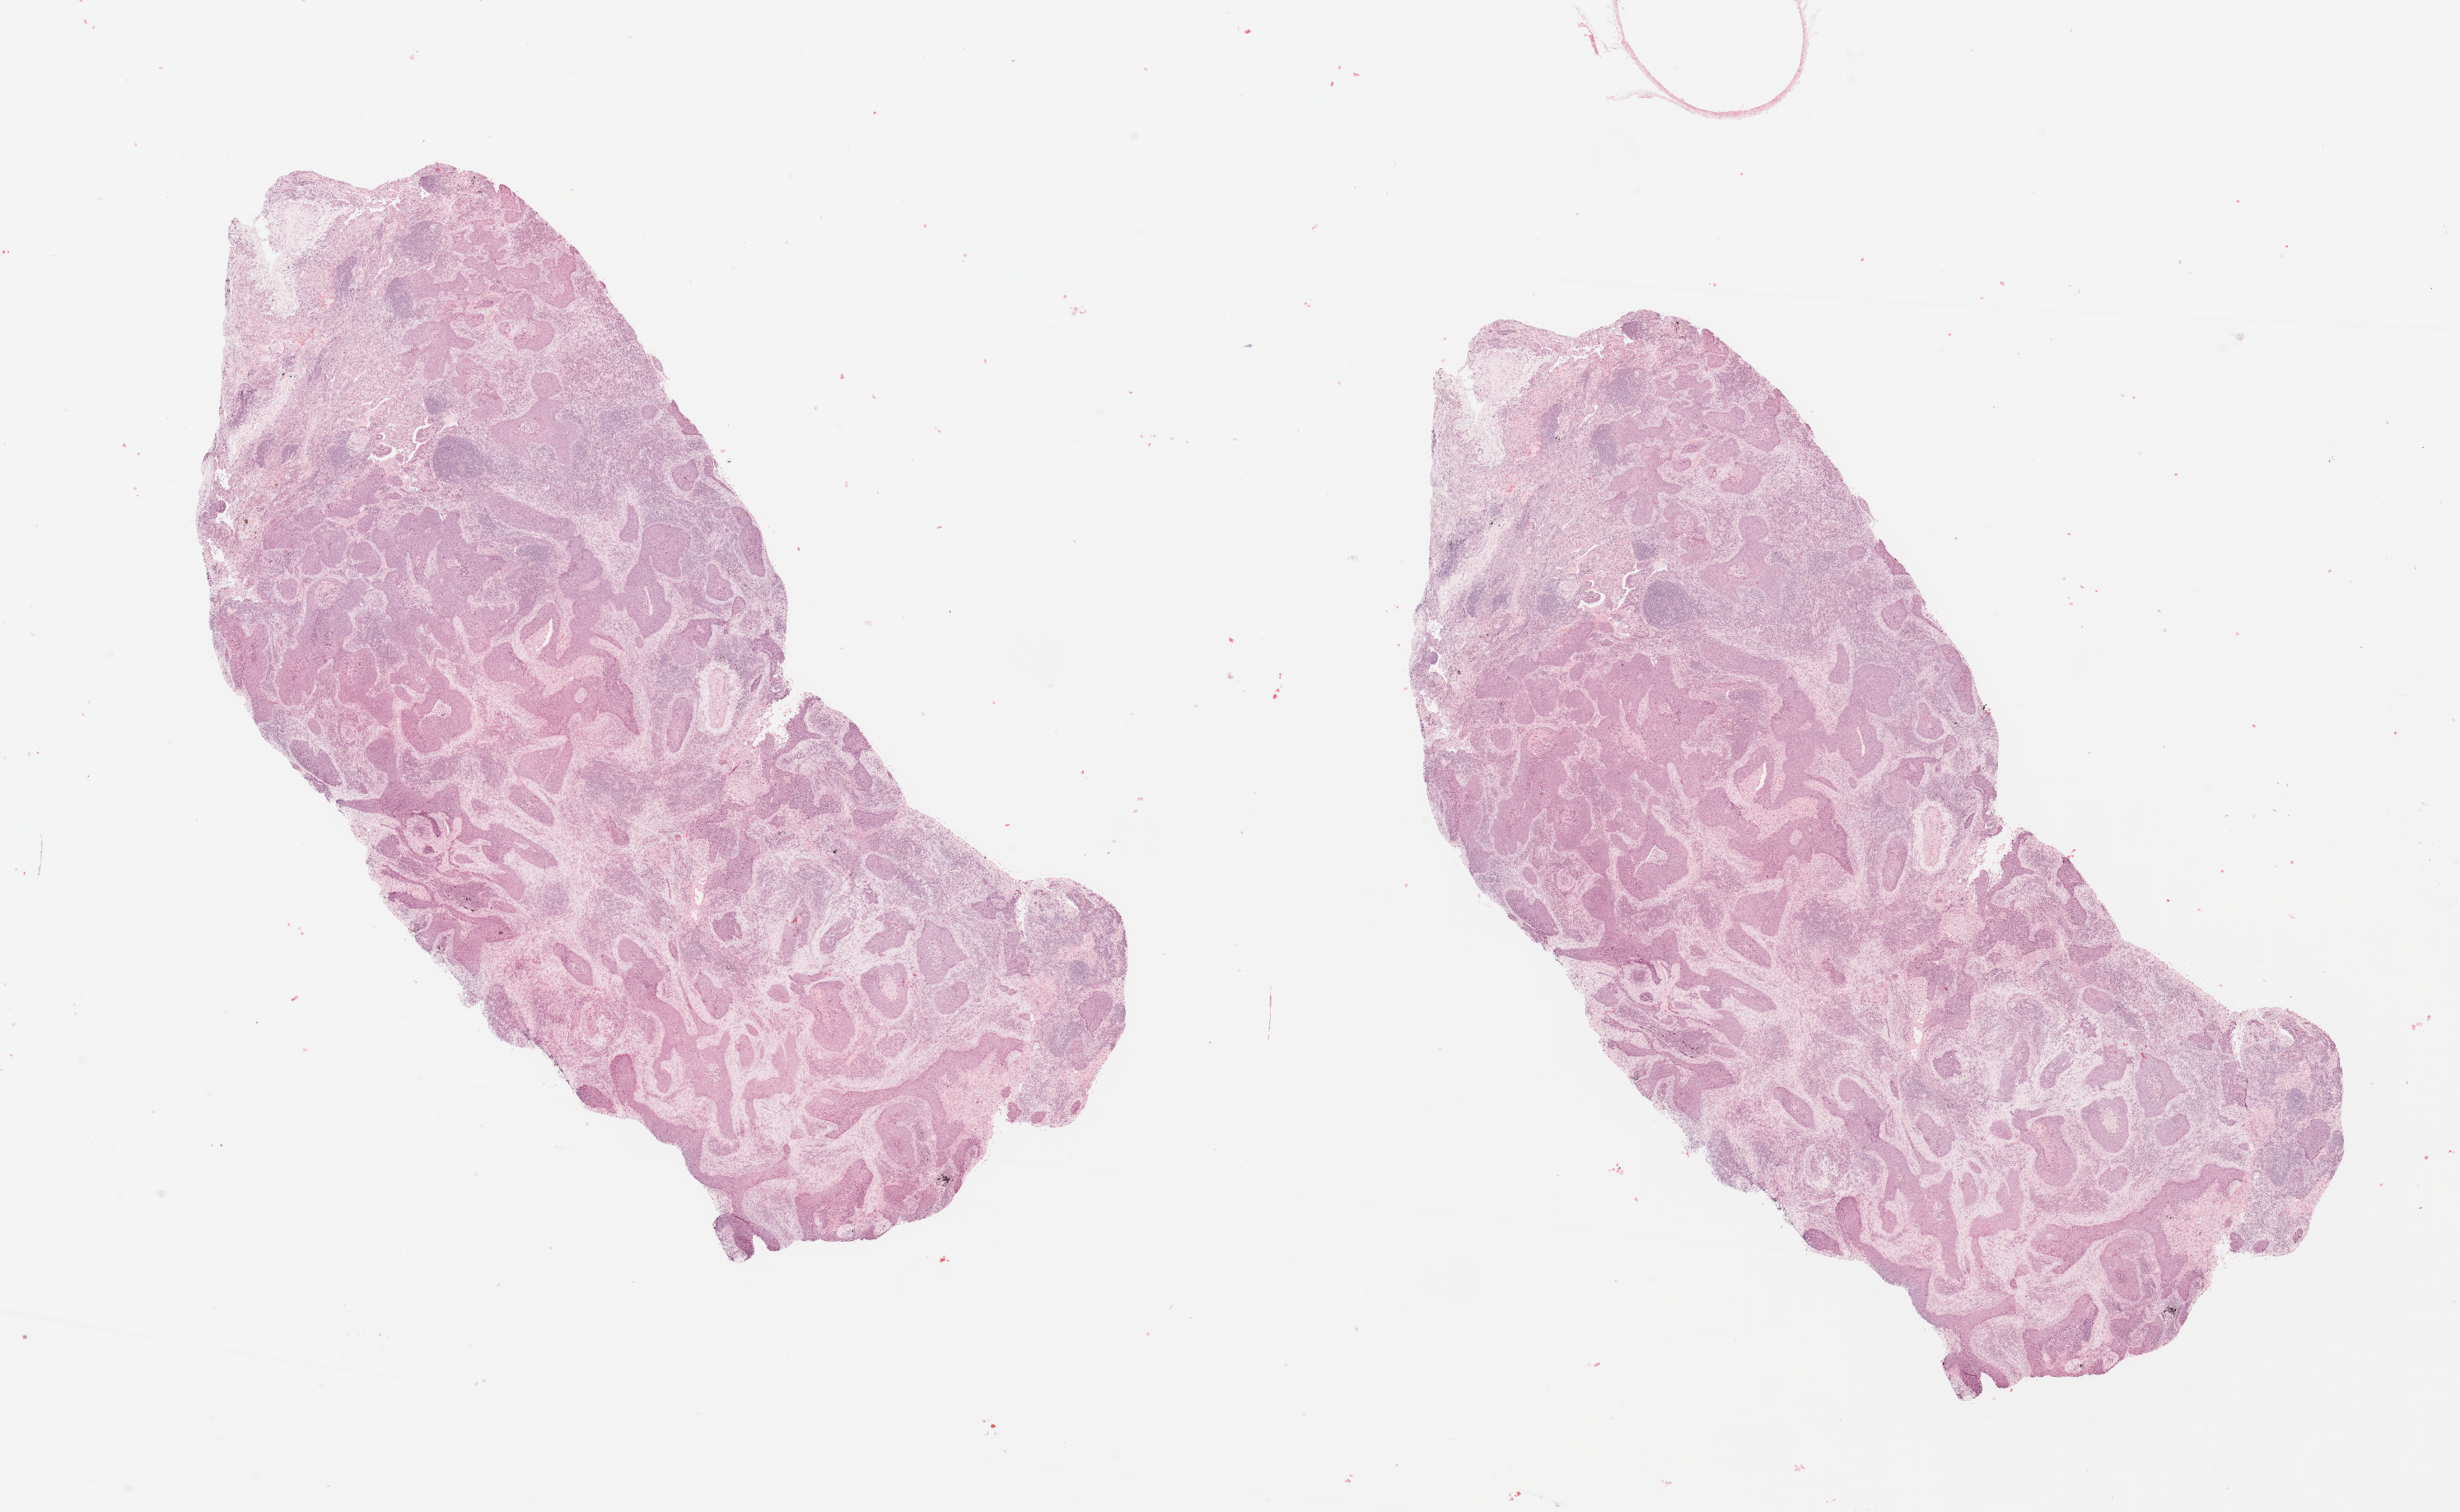
Hematoxylin and eosin (H&E) stained whole-slide image, low-resolution overview of the scanned area, about 23.6 x 14.5 mm (slide scanned at 20x). Tumour tissue sample, sampled site: lung. Patient: female, age 66 years. Histologic grade: G3 (poorly differentiated). Slide review estimates, as recorded: tumour nuclei 60%, necrosis 10%.
Diagnosis: Squamous cell carcinoma, NOS. AJCC pathologic stage: IA. Primary tumour site (as recorded): right middle lobe.